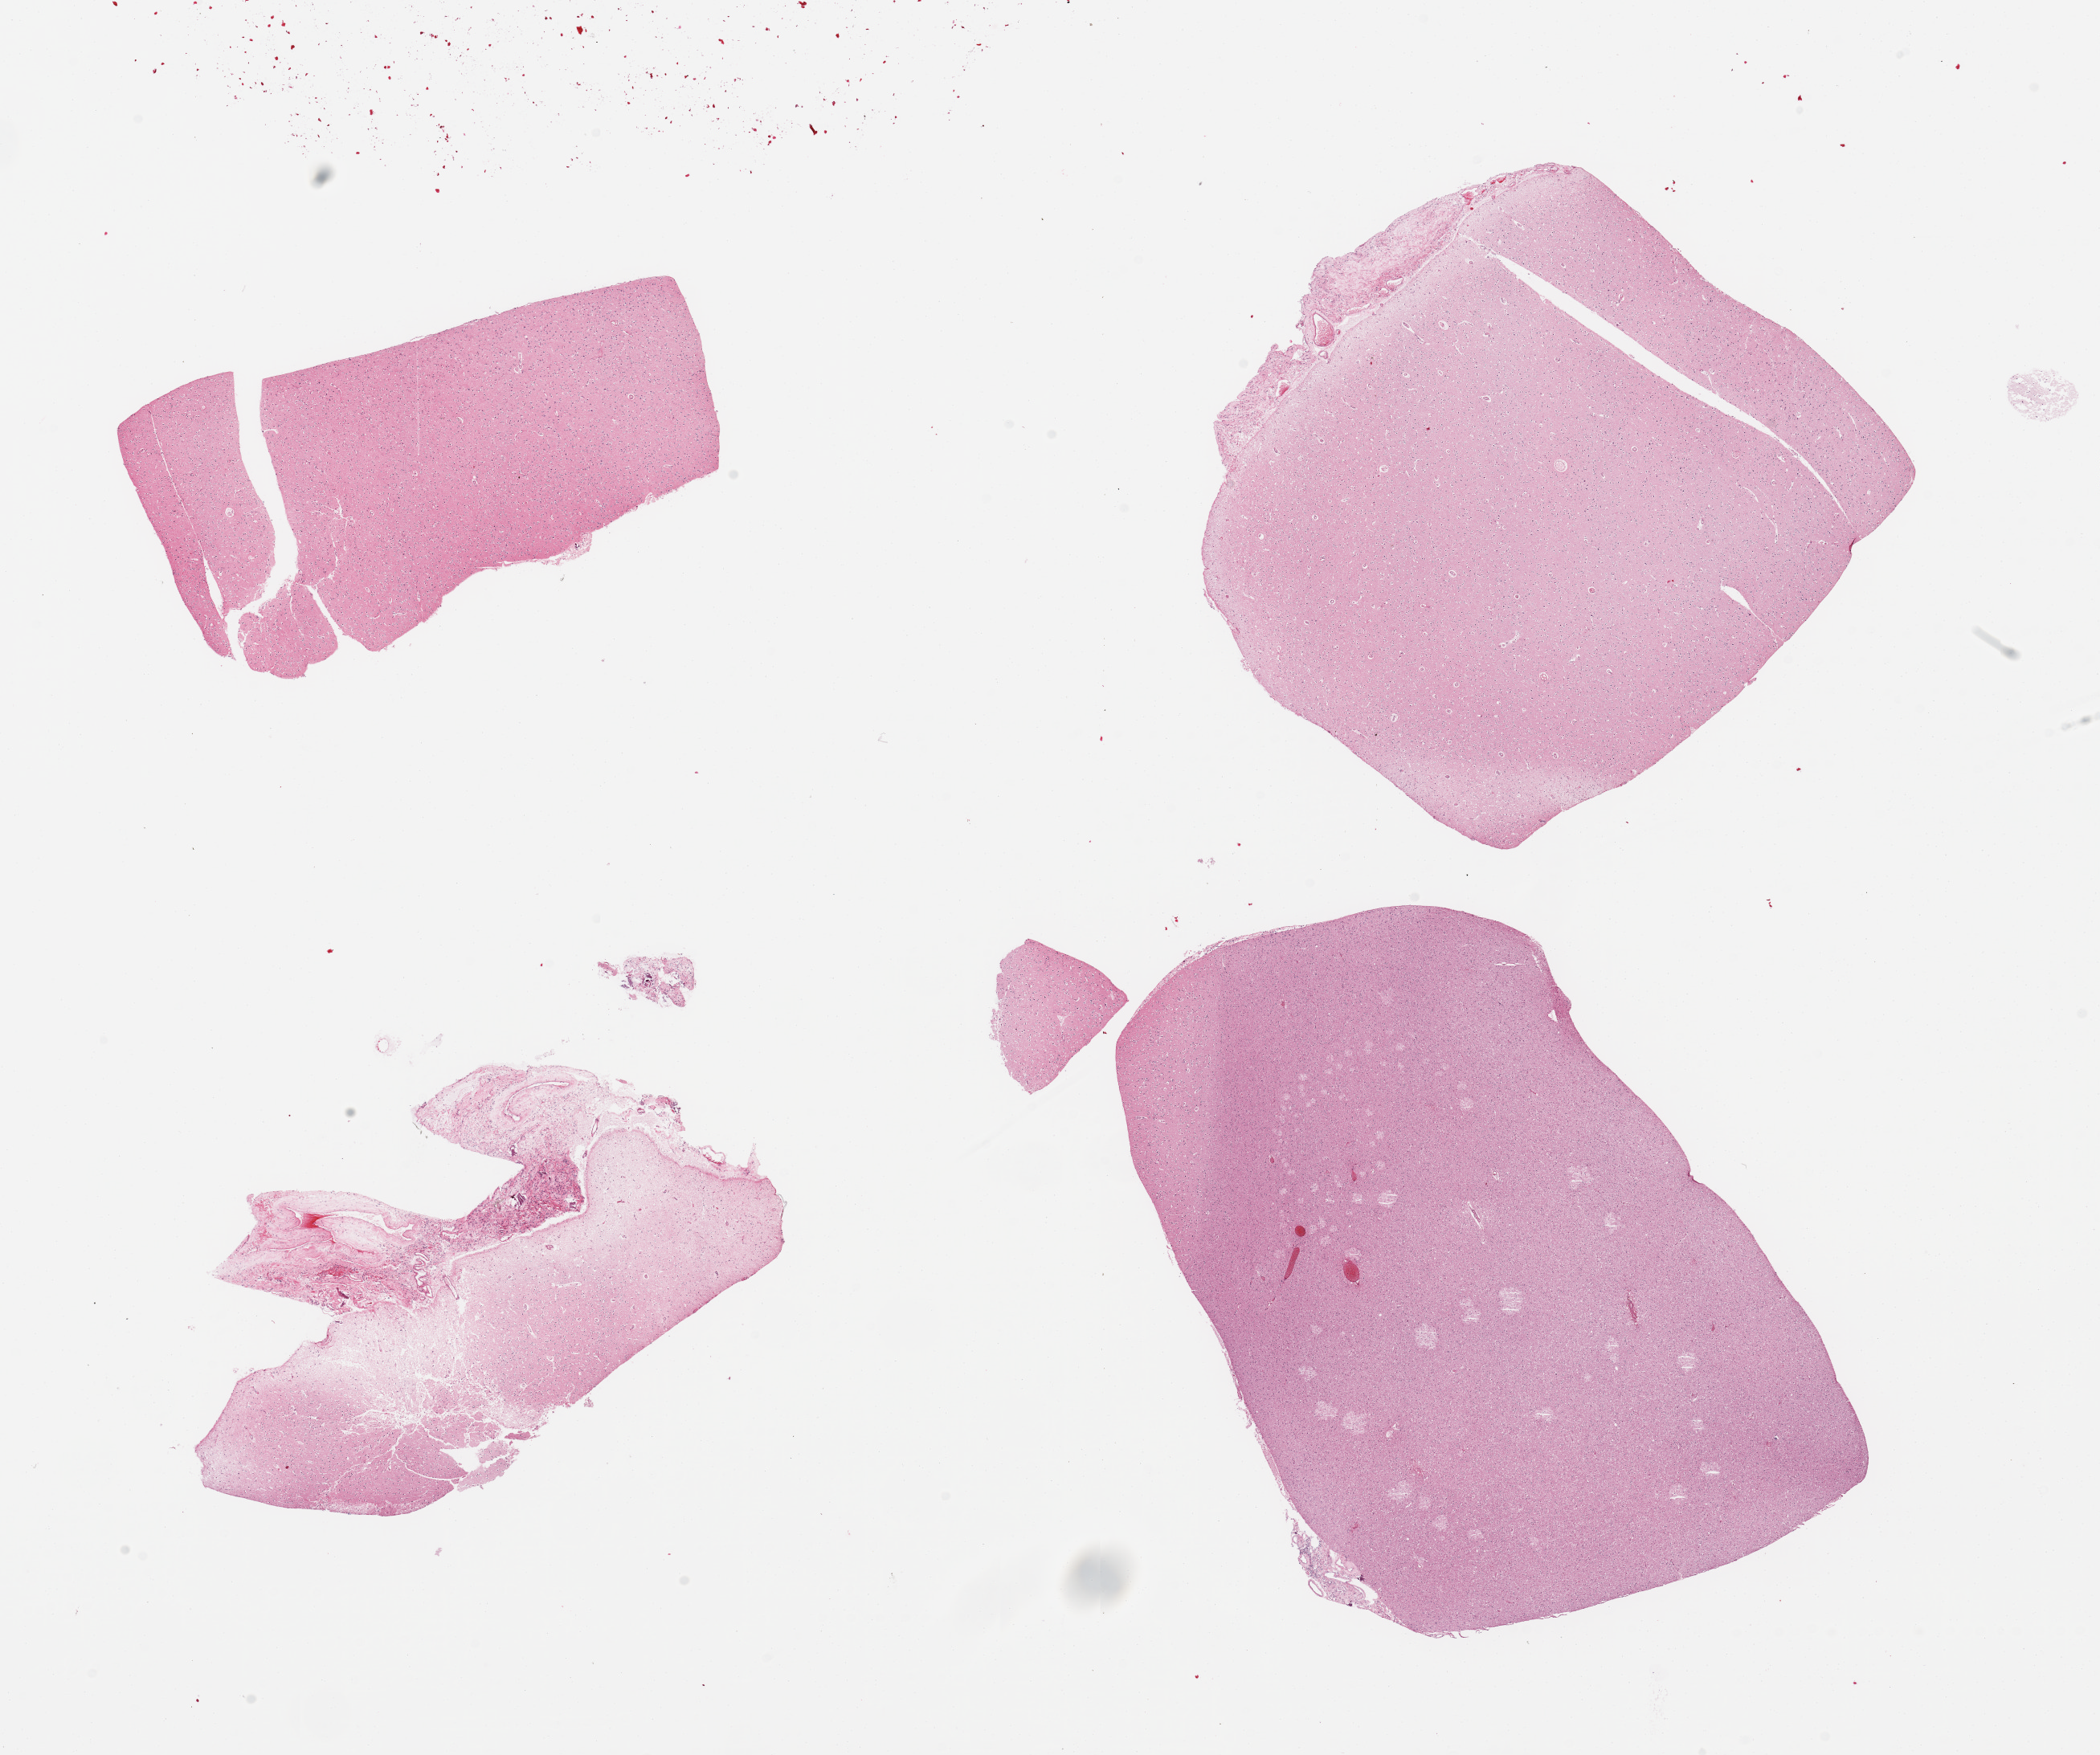
Whole-slide image, hematoxylin and eosin (H&E) stain, a low-resolution overview of the entire scanned area, about 20.7 x 17.3 mm (slide scanned at 20x). PAXgene-fixed paraffin-embedded (PFPE) section. Section of cerebral cortex (target tissue). Tissue donor sample.
- pathologist's review note for this sample: 4 pieces, fragmented; no abnormalities